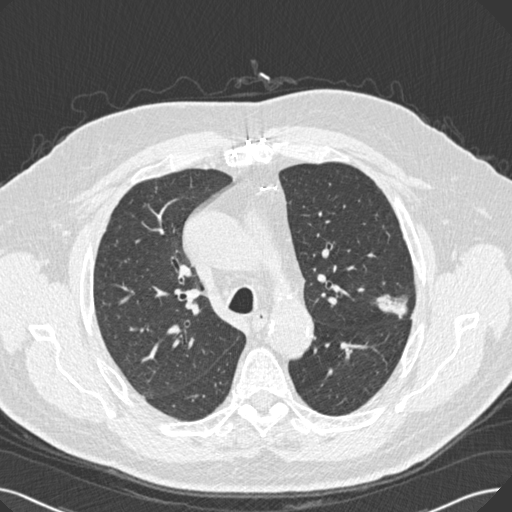
Low-dose screening chest CT, one axial slice; position 180 of 269 along the scan axis; reconstruction kernel B30f; lung window (W 1500 / L -600 HU); 512 × 512 image matrix, field of view 370 × 370 mm.
Outlined on this slice (outlined manually by an expert reader):
- lesion 1 (tumor, upper lobe of left lung): box from (x=376, y=294) to (x=407, y=319) px